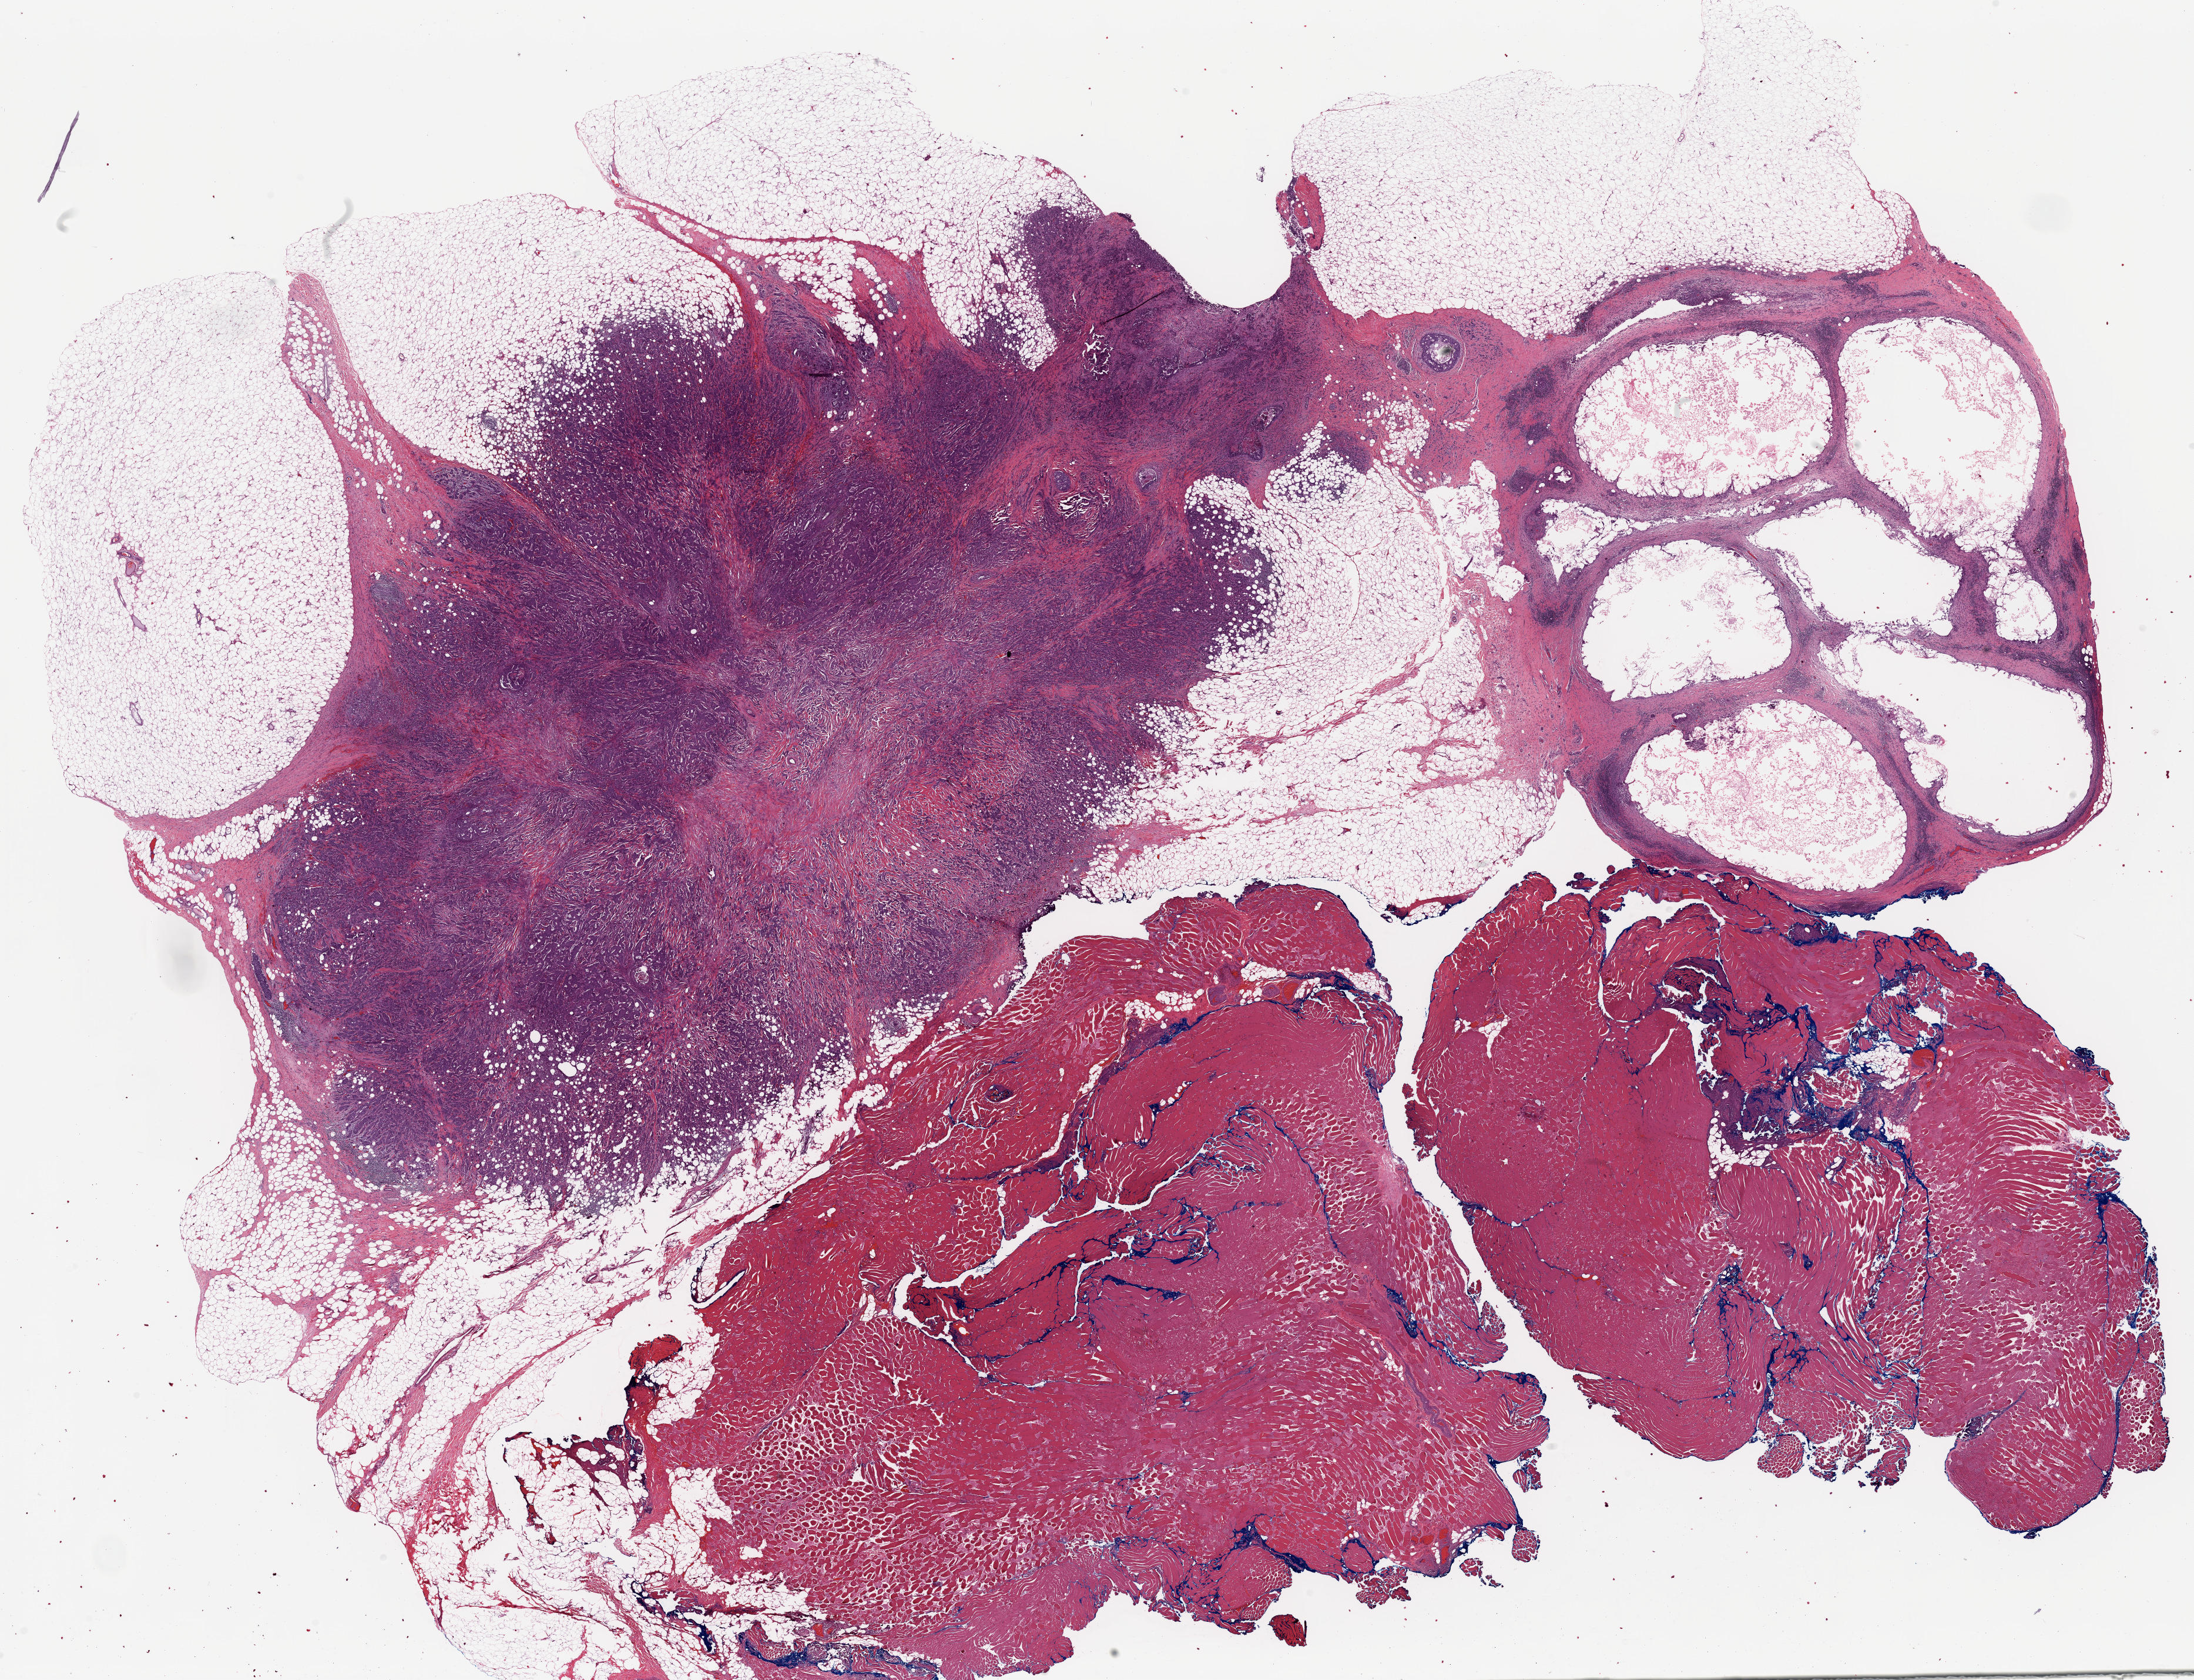
H&E-stained whole-slide image — low-resolution overview of the scanned area, about 29.8 x 22.8 mm; formalin-fixed paraffin-embedded (FFPE) diagnostic section; sample: primary tumour, breast. Female, age 40 years at initial diagnosis.
Laterality: right. AJCC pathologic stage: IIB. Diagnosis: Infiltrating duct carcinoma, NOS. Lymph nodes positive (case pathology): 2 of 23 examined.